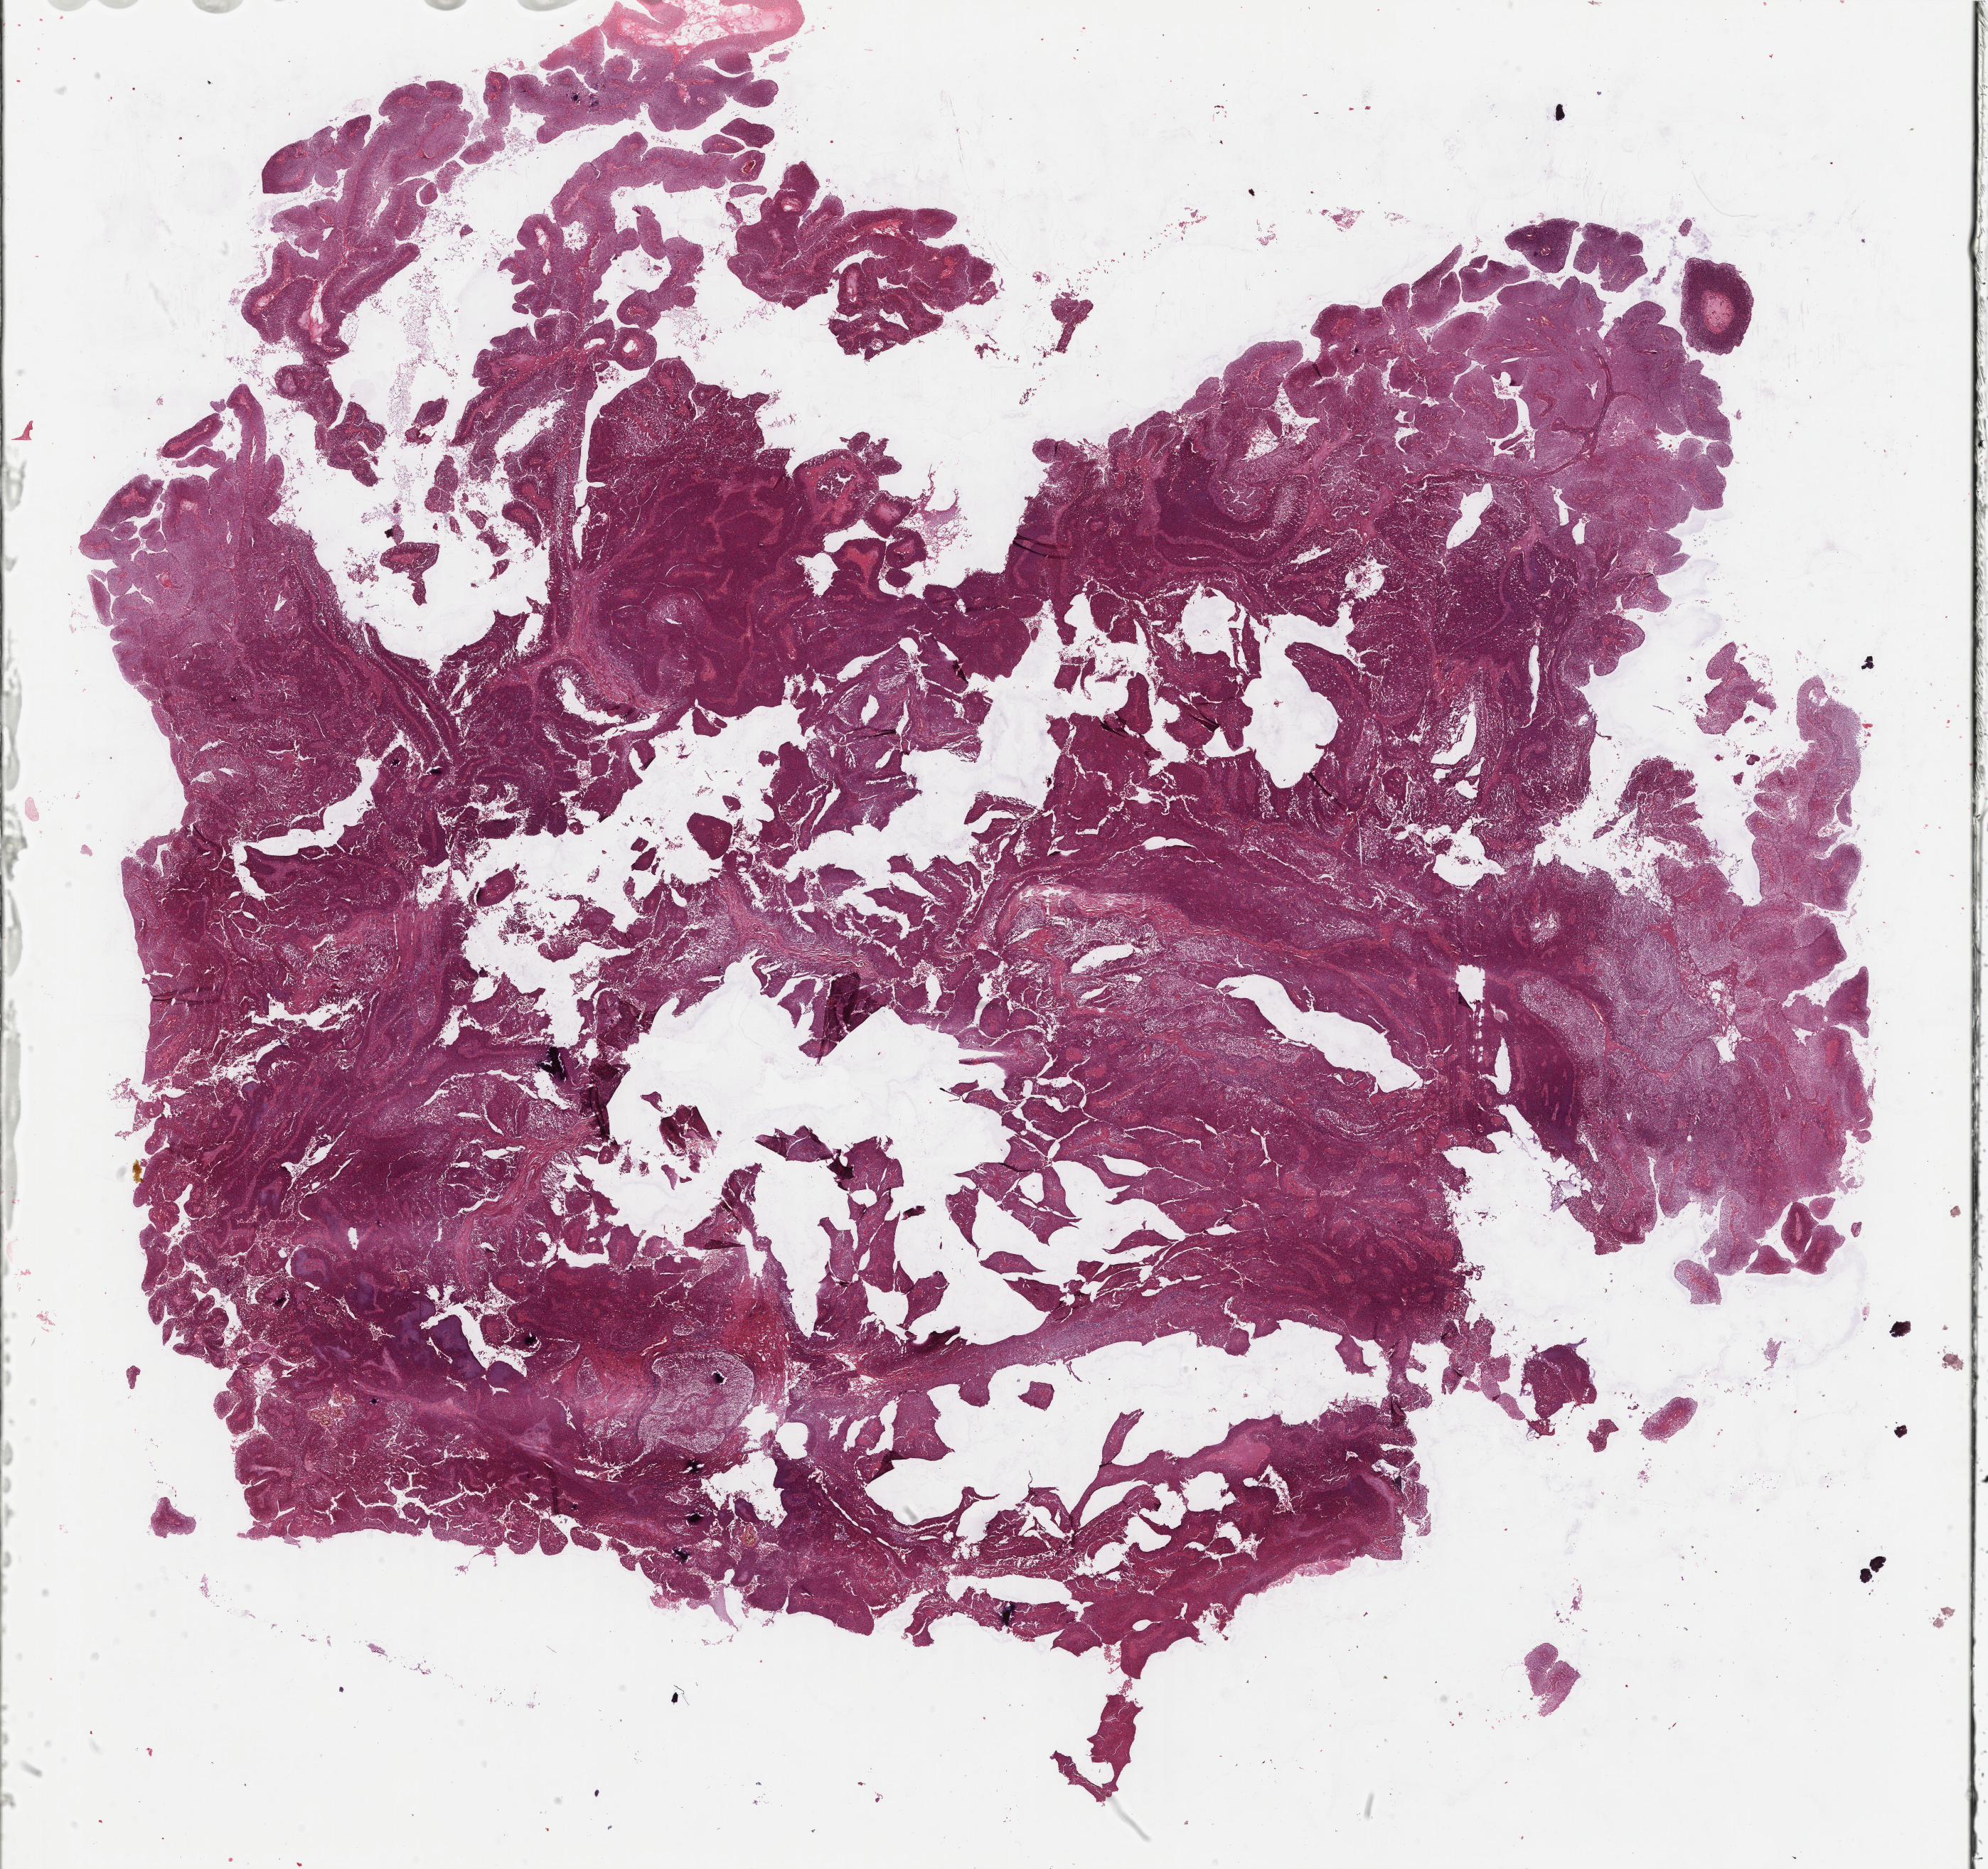
Whole-slide histology image, Hematoxylin and eosin (H&E) stained — whole scanned area (about 22.2 x 20.9 mm, from a 40x scan) shown as a low-resolution overview, formalin-fixed paraffin-embedded (FFPE) diagnostic section, bladder, primary tumour sample. Female, age 58 years at initial diagnosis. Histologic grade: low grade.
* TNM: T2 N0 M0
* AJCC pathologic stage: II (7th edition)
* histologic diagnosis: Papillary transitional cell carcinoma